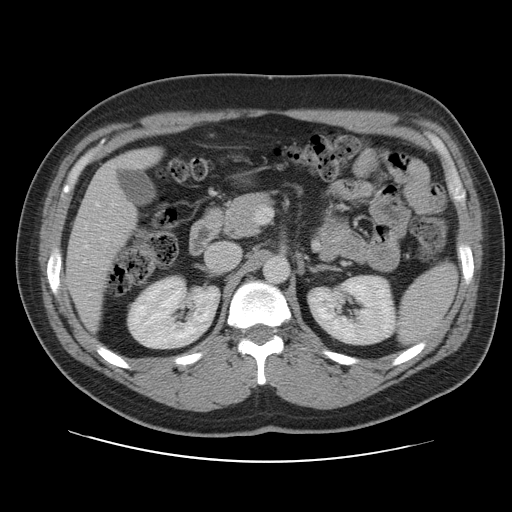
Contrast-enhanced abdominal CT, one axial slice. Position 58 of 109 along the scan axis. 120 kVp. Intravenous contrast given. Soft-tissue window (W 400 / L 40 HU). 5 mm slice thickness. 512 × 512 image matrix, field of view 402 × 402 mm. Male patient, age 35 years. Case-level facts recorded for this patient, not image findings: diagnosis: colorectal cancer liver metastases, imaged before liver resection; multiple liver metastases: yes; largest metastasis: 2.8 cm.
Outlined on this slice (outlined manually by an expert reader):
- liver: box from (x=67, y=149) to (x=160, y=327) px
- planned liver remnant (the part of the liver to remain after resection): (x=67, y=149)–(x=160, y=327)